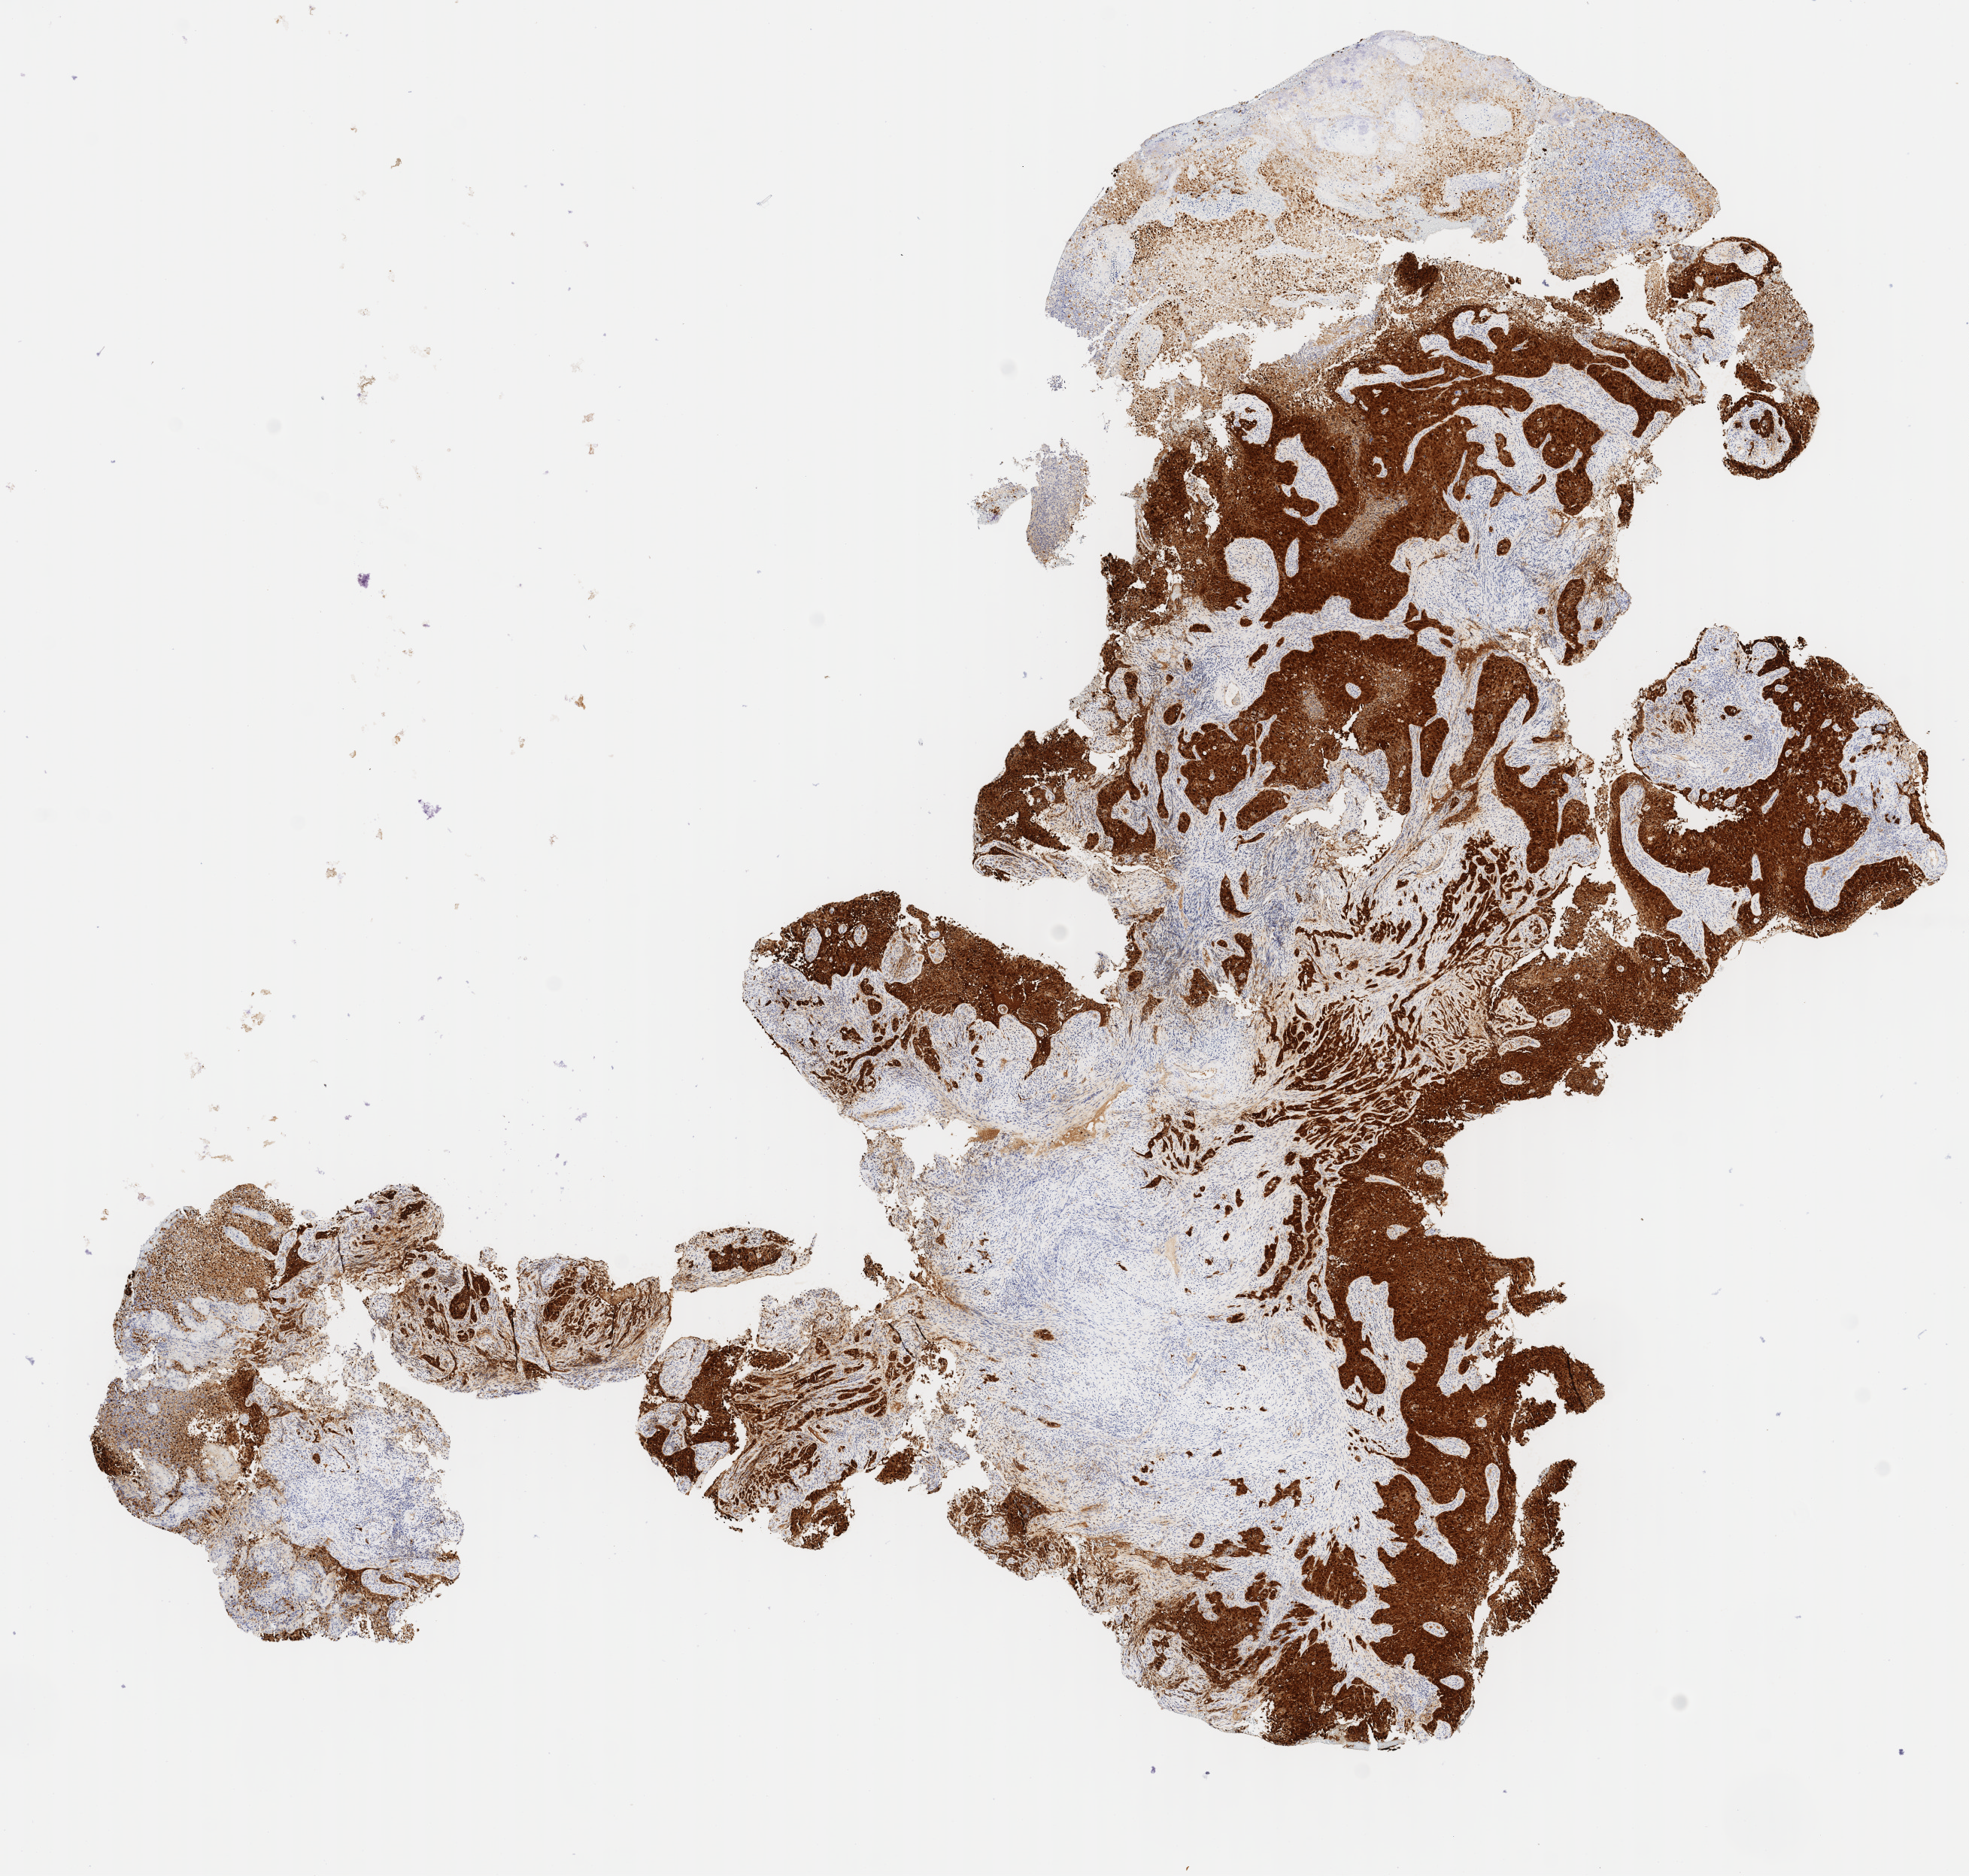
Immunohistochemistry (IHC) whole-slide image stained for p16 (p16INK4a), whole scanned area (about 10.4 x 9.9 mm) shown as a low-resolution overview, tumor tissue, anatomic site: cervix. Patient sex: female.
Diagnosis: Squamous cell carcinoma, large cell, nonkeratinizing, NOS.